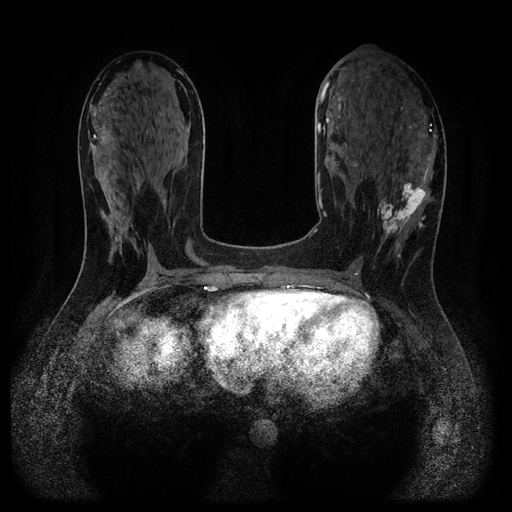
Breast MRI (dynamic contrast-enhanced, multi-phase), one axial slice. Position 51 of 116 along the scan axis. Dynamic contrast-enhanced series, time point 2 of 5 at this slice position (early post-contrast). 1.5 T. TE 2.7 ms, TR 5.4 ms. 2.2 mm slice thickness. 512 × 512 image matrix, field of view 330 × 330 mm. Female patient, age 43 years.
Structures marked on this image (semi-automatic segmentation, software-assisted and operator-edited):
- breast lesion (labelled 'tumour' in the annotation; benign lesions carry a separate 'benign' label): bounding box [x1, y1, x2, y2] px = [377, 181, 430, 246]
- breast lesion (labelled benign in the annotation): [134, 60, 143, 72]